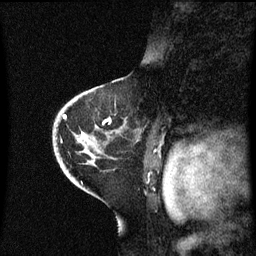
Breast MRI (dynamic contrast-enhanced), one sagittal slice. Slice 39 of 60 in the series (ordered by position). Dynamic contrast-enhanced series, image 2 of 3 at this slice position (ordered by acquisition). 1.5 T. TE 4.2 ms, TR 8.4 ms. 2.3 mm slice thickness. 256 × 256 image matrix. Patient: female, 46 years. Case-level facts recorded for this patient, not image findings: setting: breast cancer imaged before/during neoadjuvant chemotherapy; receptor status: HER2-positive.
Outlined on this slice (semi-automatic segmentation, software-assisted and operator-edited):
- analysis volume of interest (the breast-tissue region the enhancement analysis was run in; not a lesion): box from (x=54, y=86) to (x=127, y=171) px
- tumour enhancement mask (voxels above the 70 % enhancement threshold inside the analysis volume of interest): (x=64, y=116)–(x=85, y=139)